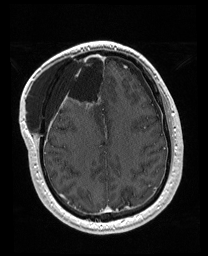
Brain MRI from a brain-tumour surgery series, one axial slice. Slice 64 of 176 in the series (ordered by position). T1-weighted post-contrast. 1 mm slice thickness. 208 × 256 image matrix, field of view 208 × 256 mm. Case-level facts recorded for this patient, not image findings: histopathology: Astrocytoma; WHO grade: 4; IDH mutation: yes.
Outlined on this slice (expert manual segmentation):
- previous resection cavity: box from (x=56, y=52) to (x=106, y=111) px